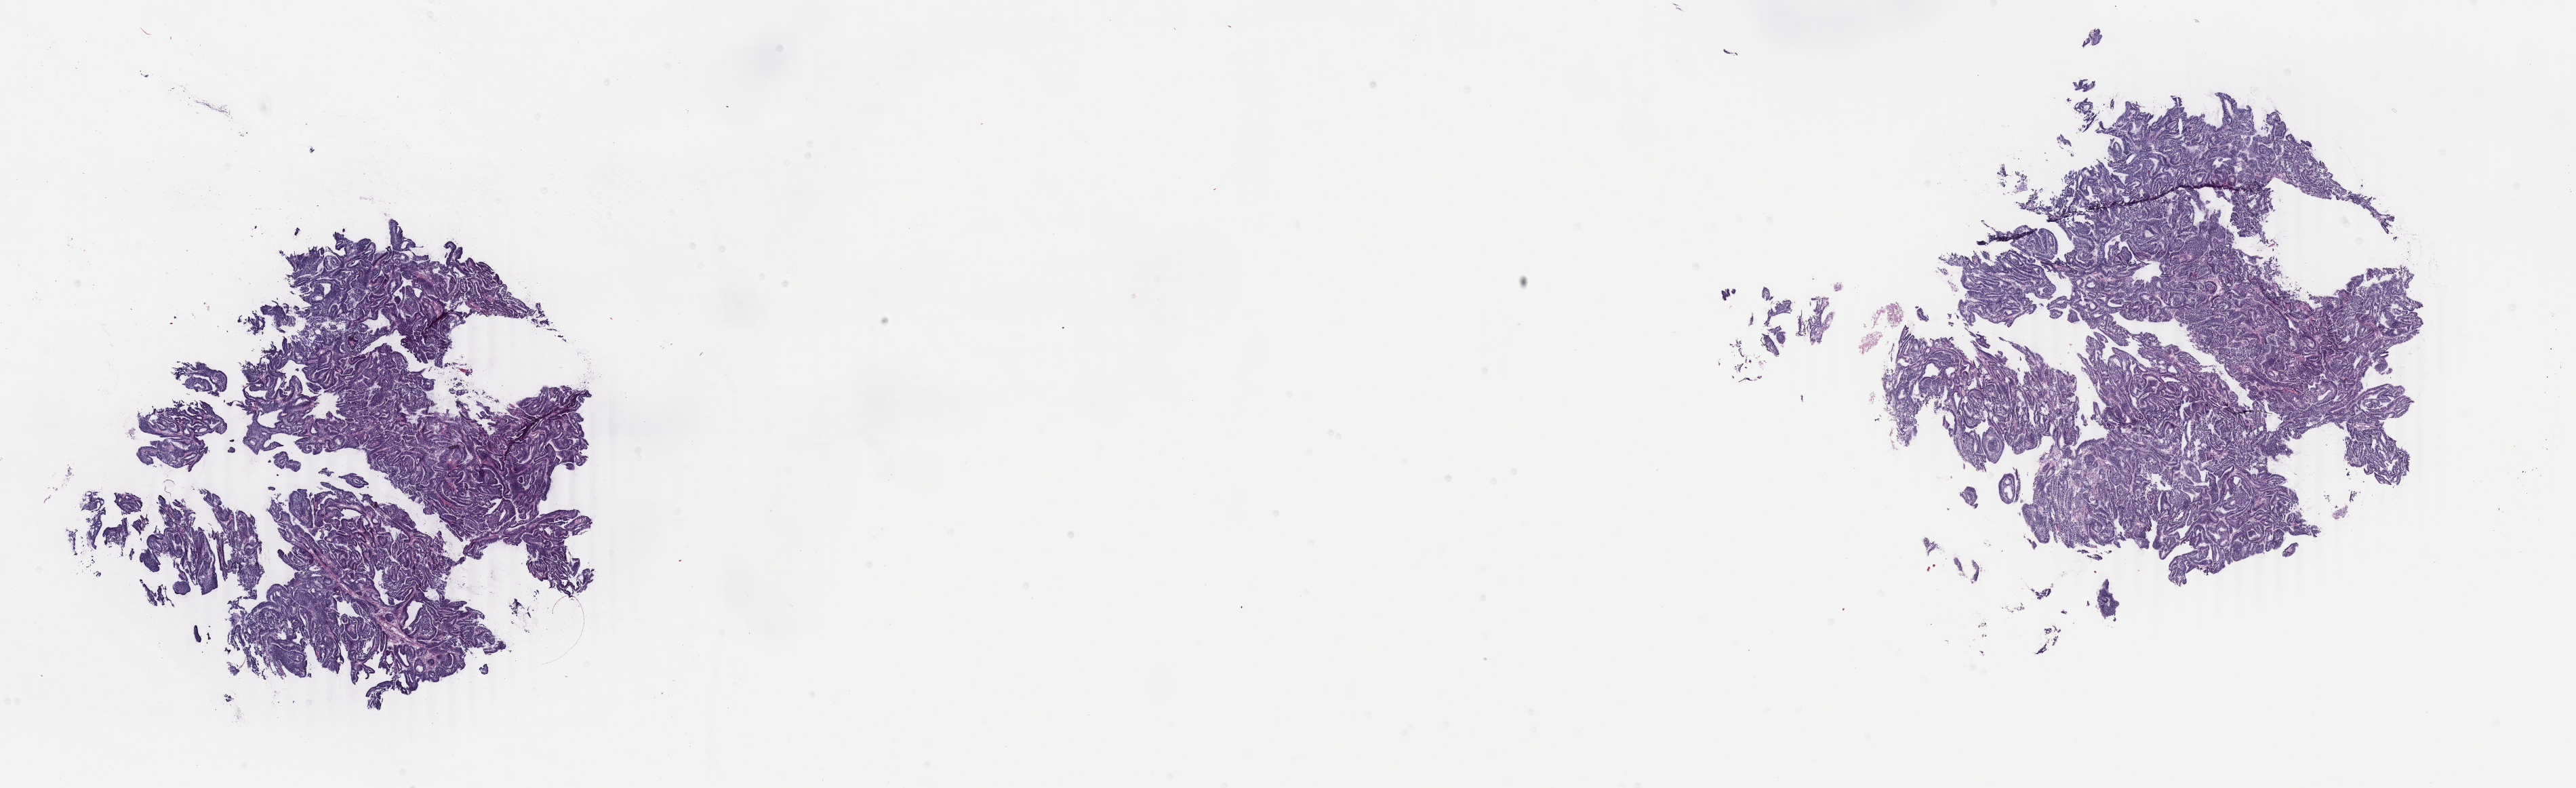
Whole-slide histology image, H&E-stained — whole scanned area (about 30.2 x 9.2 mm) shown as a low-resolution overview; frozen section from the top of the tissue portion; uterus, primary tumour sample. Patient: female, age at initial diagnosis 63 years. Histologic grade: G1 (well differentiated). Pathologist review of this section (percent, as recorded): tumour cells 96%, tumour nuclei 97%, normal cells 0%, stromal cells 3%, necrosis 1%. Infiltration values recorded for this section: lymphocyte infiltration 1%, monocyte infiltration 0%, neutrophil infiltration 0%.
- FIGO stage: IA
- histologic diagnosis: Endometrioid adenocarcinoma, NOS (endometrium)